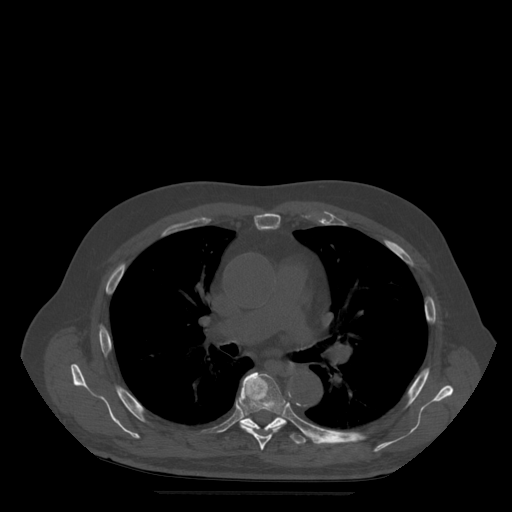
CT including the spine, one axial slice. Position 346 of 522 along the scan axis. Bone window (W 1800 / L 400 HU). 1.25 mm slice thickness. 512 × 512 image matrix. Patient age 72 years. Case-level facts recorded for this patient, not image findings: primary cancer: prostate.
Outlined on this slice (semi-automatically segmented with operator editing):
- T6 vertebra: bounding box [x1, y1, x2, y2] px = [239, 372, 287, 451]
- T7 vertebra: [241, 417, 307, 445]